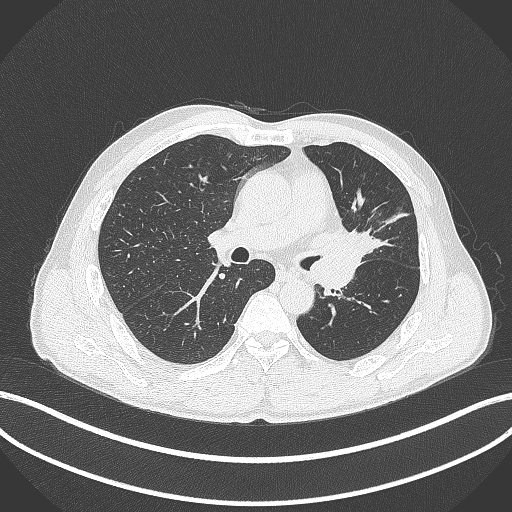
Chest CT, one axial slice. Position 244 of 429 along the scan axis. Lung window (W 1500 / L -600 HU). 1 mm slice thickness. 512 × 512 image matrix. Patient: male, 57 years. From the clinical record (not read from this slice): clinical TNM (as recorded): T2b N0 M0.
Annotated regions visible in this slice (bounding box drawn by a radiologist):
- lung tumour (recorded histology: squamous cell carcinoma): box from (x=322, y=230) to (x=373, y=265) px